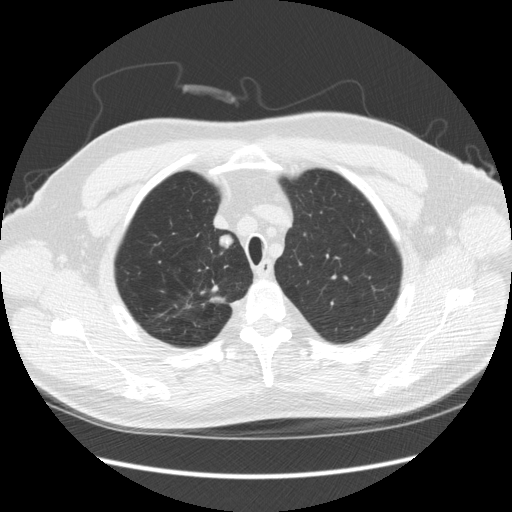
Low-dose screening chest CT, axial slice, third screening round (two years after baseline), lung window (W 1500 / L -600 HU), slice 36 of 248 in the series. Male participant, aged 64 years at enrolment. Former smoker at enrolment.
2 expert-annotated lung lesions on this slice (largest first), box from (x=201, y=230) to (x=242, y=259) px; (x=201, y=280)–(x=233, y=312). The screening reader recorded 4 non-calcified nodules or masses ≥4 mm on this exam; which of them these boxes mark is not recorded. Official screen result: positive, other.